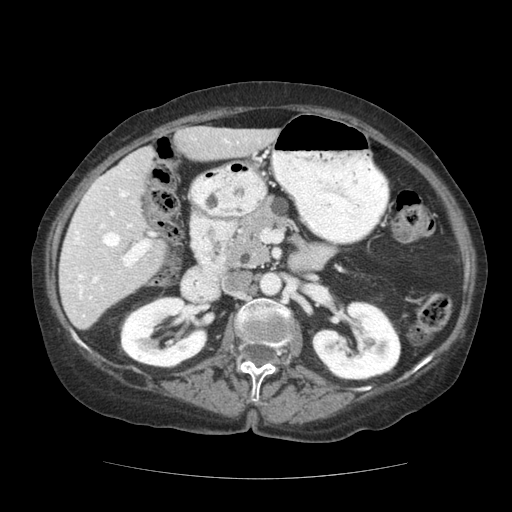
Contrast-enhanced abdominal CT (liver protocol), one axial slice; position 62 of 111 along the scan axis; soft-tissue window (W 400 / L 40 HU); 512 × 512 image matrix, field of view 360 × 360 mm. Case-level facts recorded for this patient, not image findings: diagnosis: hepatocellular carcinoma (patient treated with transarterial chemoembolisation; whether this scan precedes or follows treatment is not stated here); TNM stage (as recorded): Stage-I; Child-Pugh class: A; tumour nodularity: uninodular.
Structures marked on this image (semi-automatically segmented with operator editing):
- liver parenchyma outside the tumour (the mass and vessels are separate outlines, so this box may not span the whole liver): bounding box (x1, y1, x2, y2) in pixels: (60, 126, 278, 329)
- liver vessels: (64, 139, 230, 317)